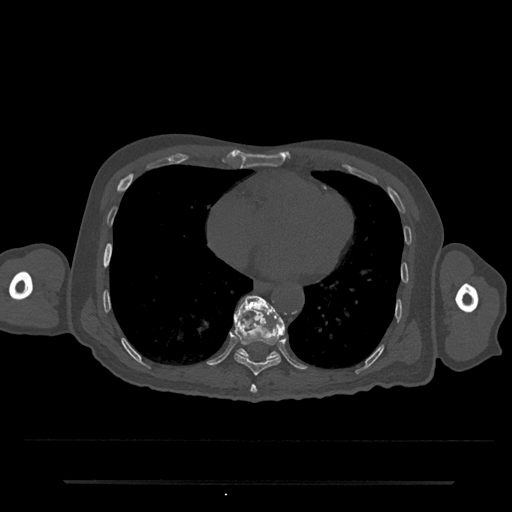
CT including the spine, one axial slice; slice 352 of 797 in the series (ordered by position); reconstruction kernel Br40s/3; bone window (W 1800 / L 400 HU); 0.5 mm slice thickness; 512 × 512 image matrix, field of view 427 × 427 mm. Male patient, age 74 years. Case-level facts recorded for this patient, not image findings: primary cancer: prostate.
Outlined on this slice (semi-automatic segmentation, software-assisted and operator-edited):
- T10 vertebra: bounding box [x1, y1, x2, y2] px = [236, 295, 285, 361]
- T8 vertebra: [250, 385, 257, 393]
- T9 vertebra: [234, 296, 285, 376]